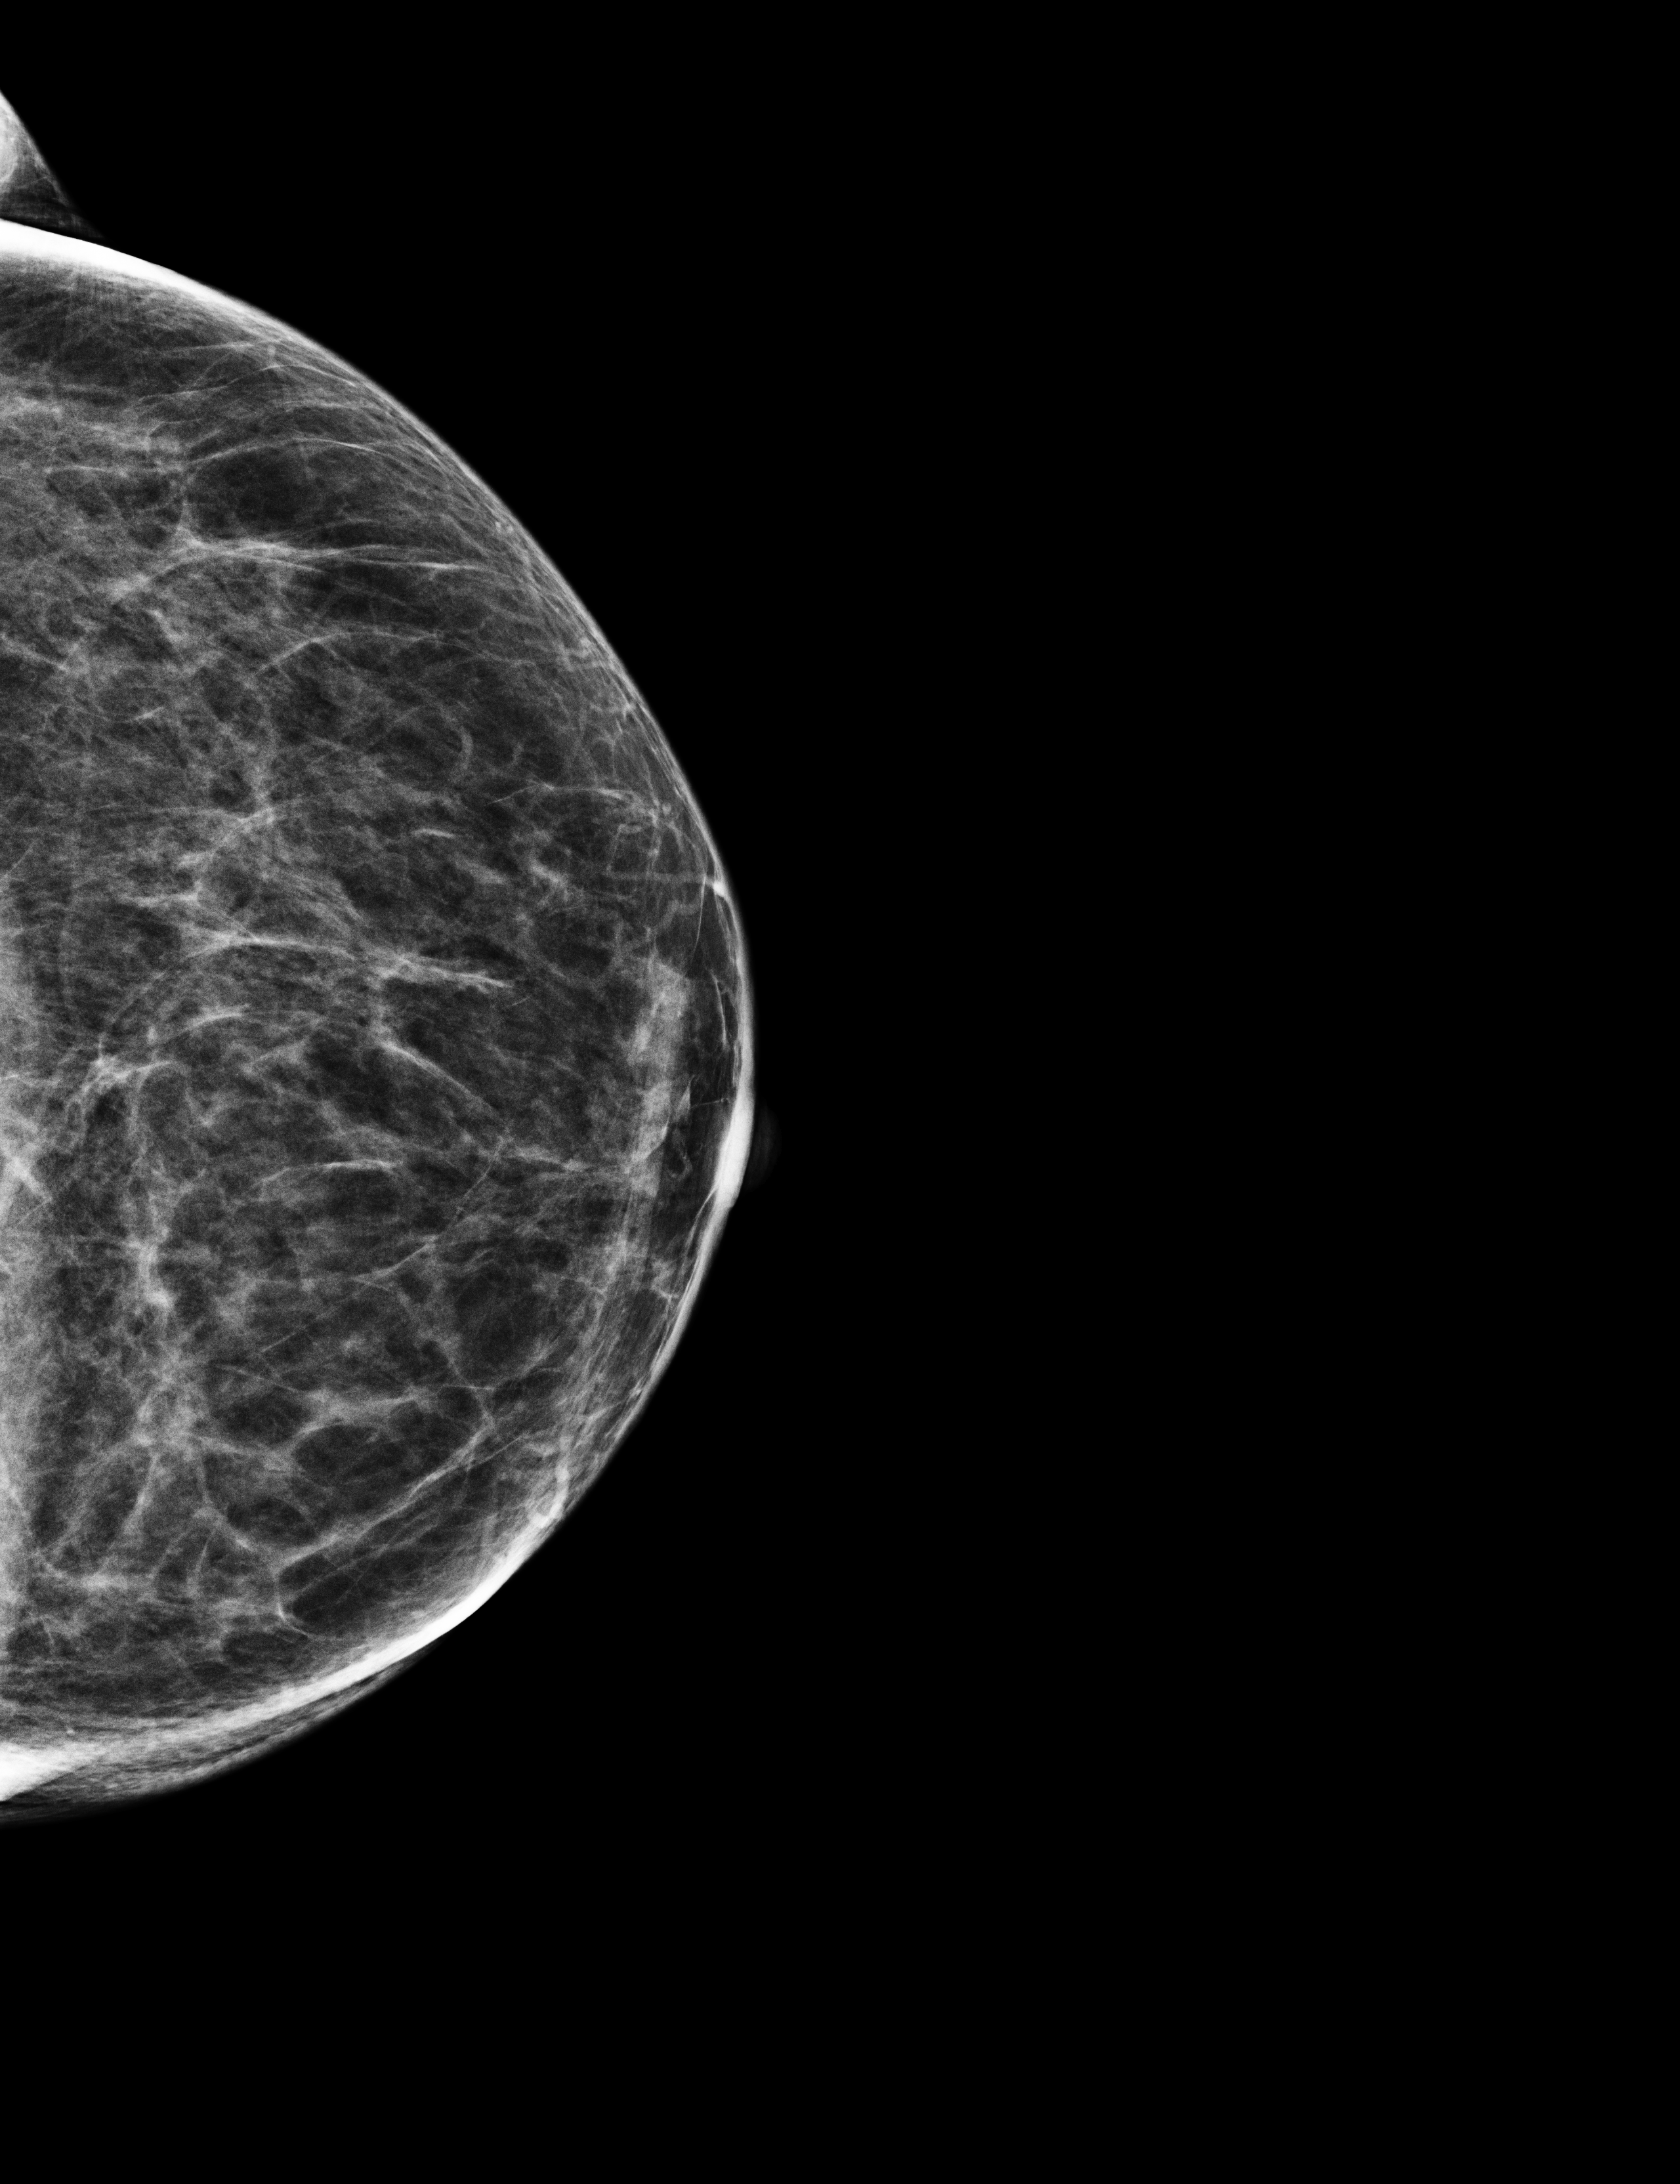
Digital mammogram (FFDM); left breast; craniocaudal (CC) view; screening examination; system: Selenia Dimensions. Patient: female, 64 years.
- BI-RADS breast density category at the screening exam (both breasts, scale 1–4): 3
- final BI-RADS category for the screening round (tomosynthesis exam, both breasts): category 1
- recall: no recall after this screen